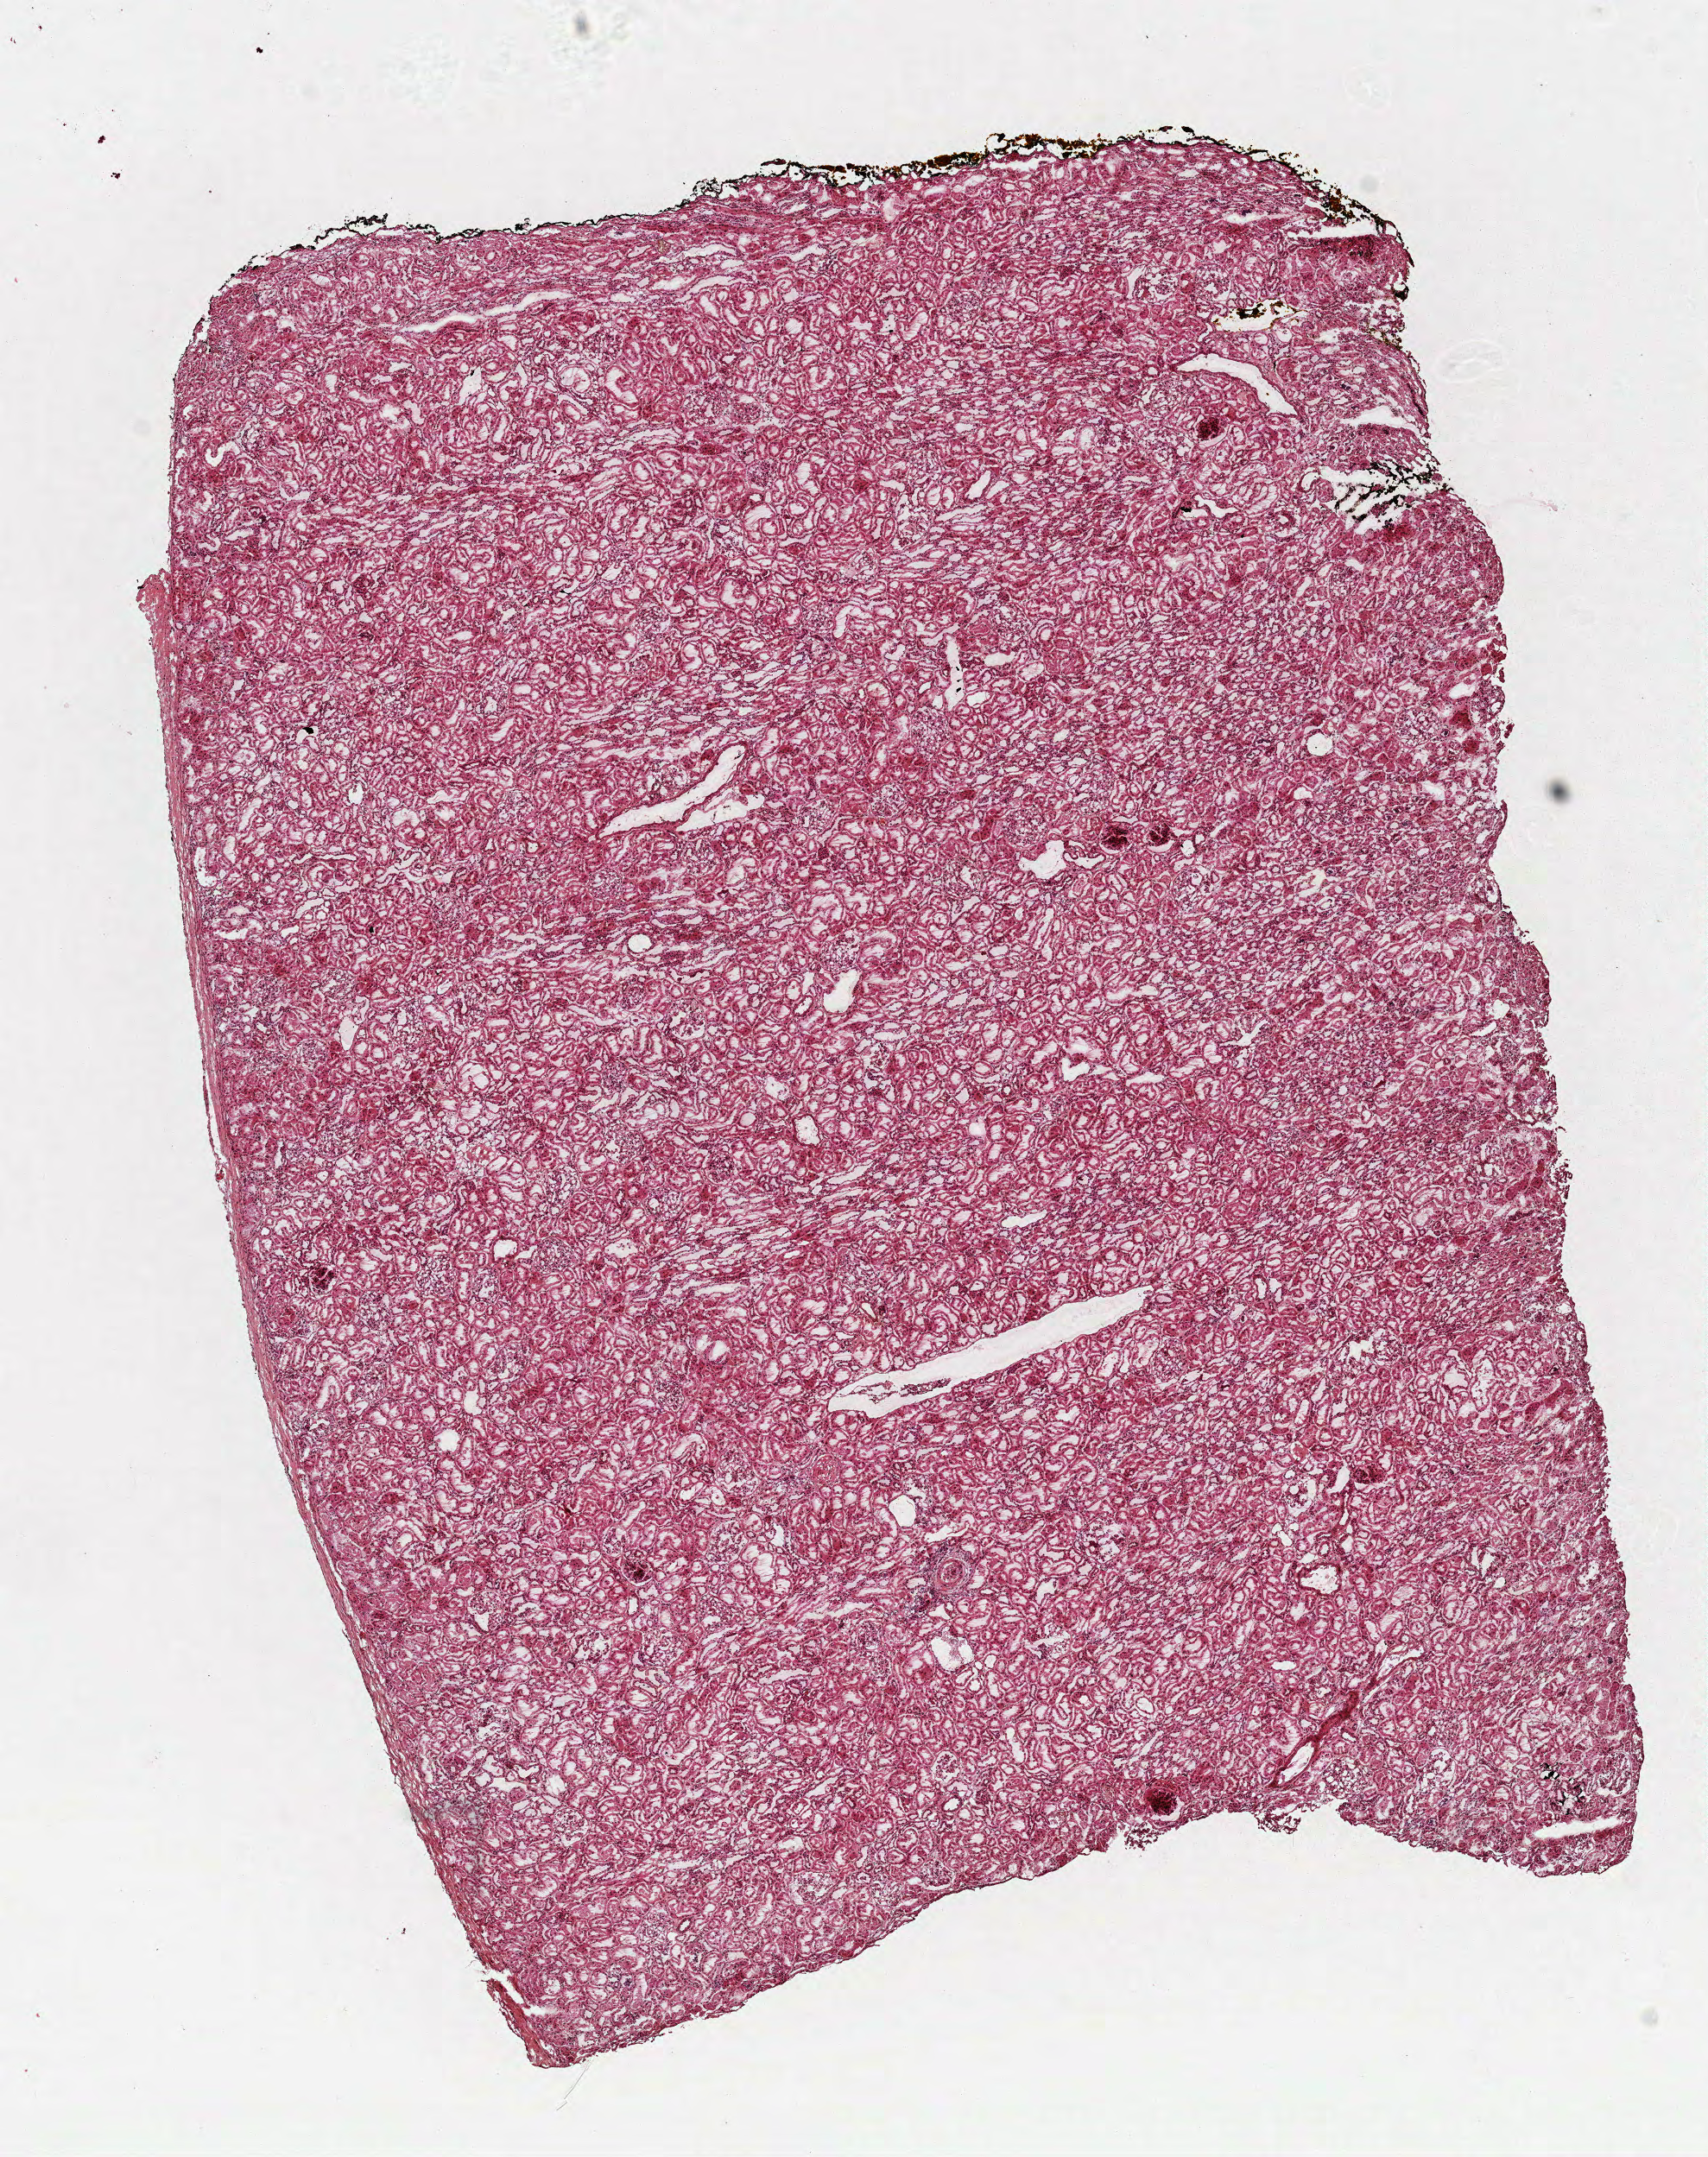
Hematoxylin and eosin (H&E) stained whole-slide image — low-resolution overview of the scanned area, about 8.0 x 10.1 mm; frozen section from the top of the tissue portion; kidney, solid tissue normal (non-tumour tissue) sample. Patient: female, age at initial diagnosis 57 years.
• this section: solid tissue normal (non-tumour) sample from the same patient
• patient diagnosis: Papillary adenocarcinoma, NOS